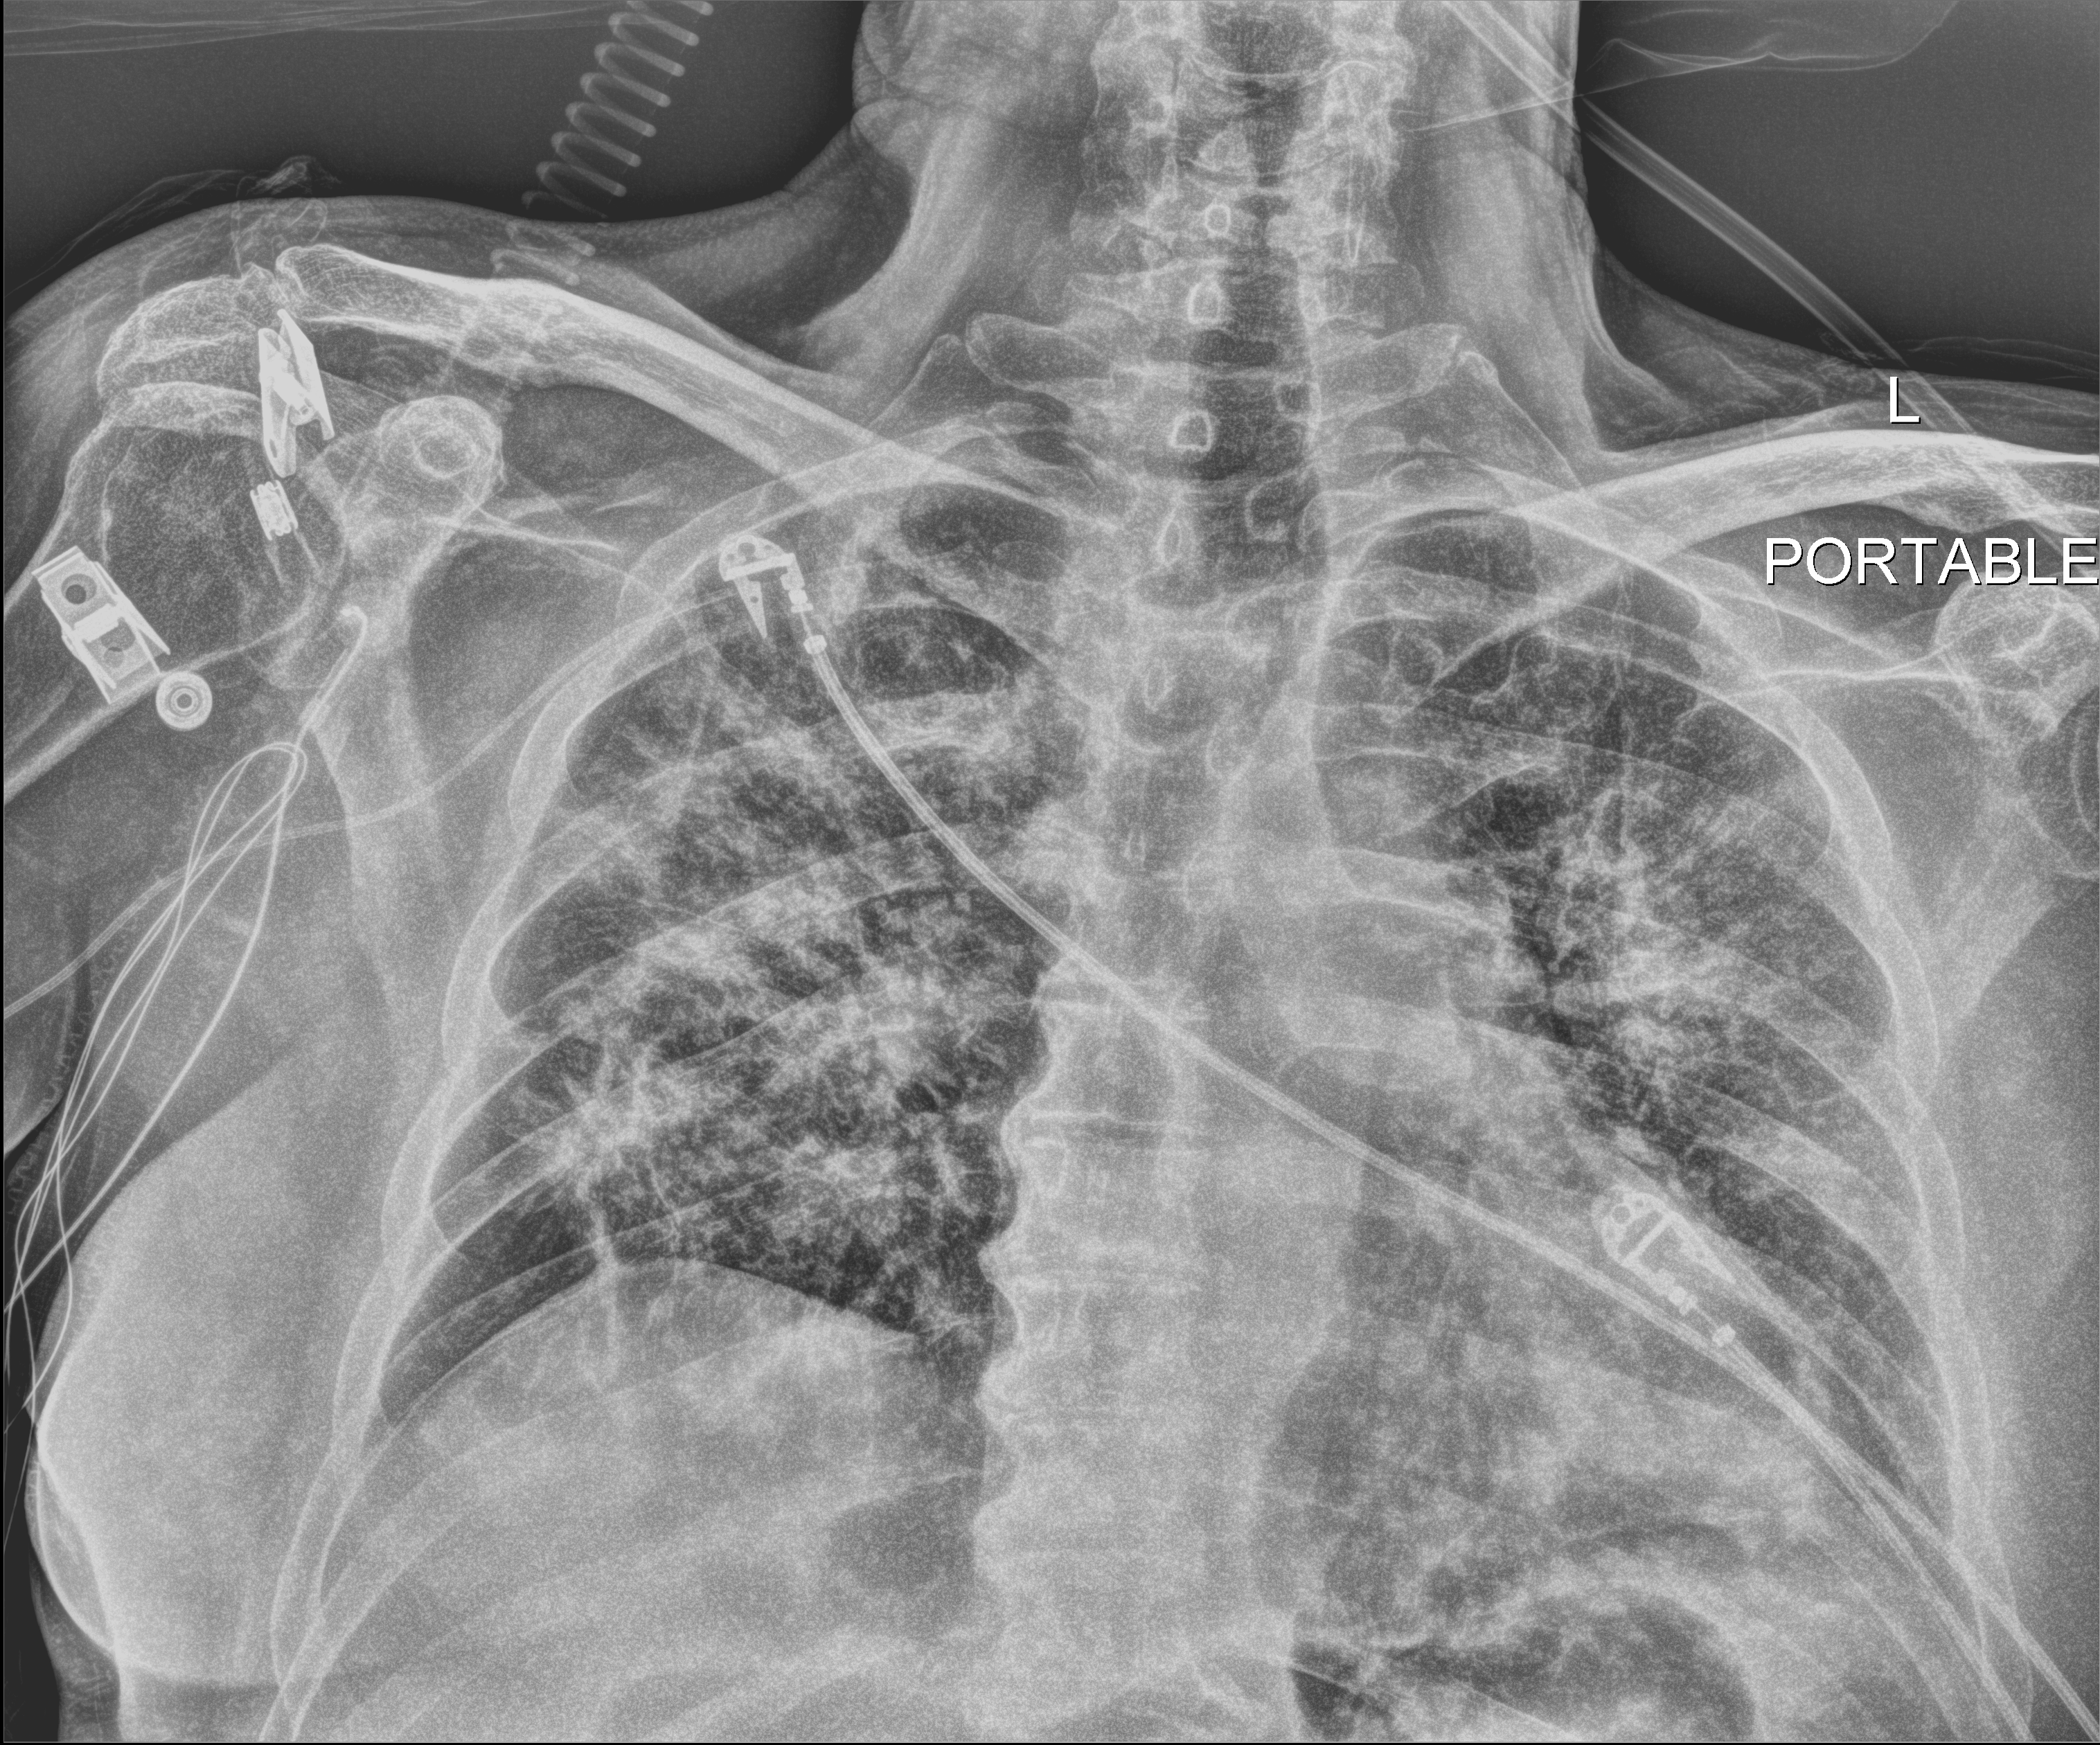
Portable chest radiograph, anteroposterior (AP) projection. Male patient hospitalised with COVID-19, age 60–74 years.
Admission-level facts for this patient (not findings on this image; timing relative to this image not recorded): mechanically ventilated during this hospital stay: no.